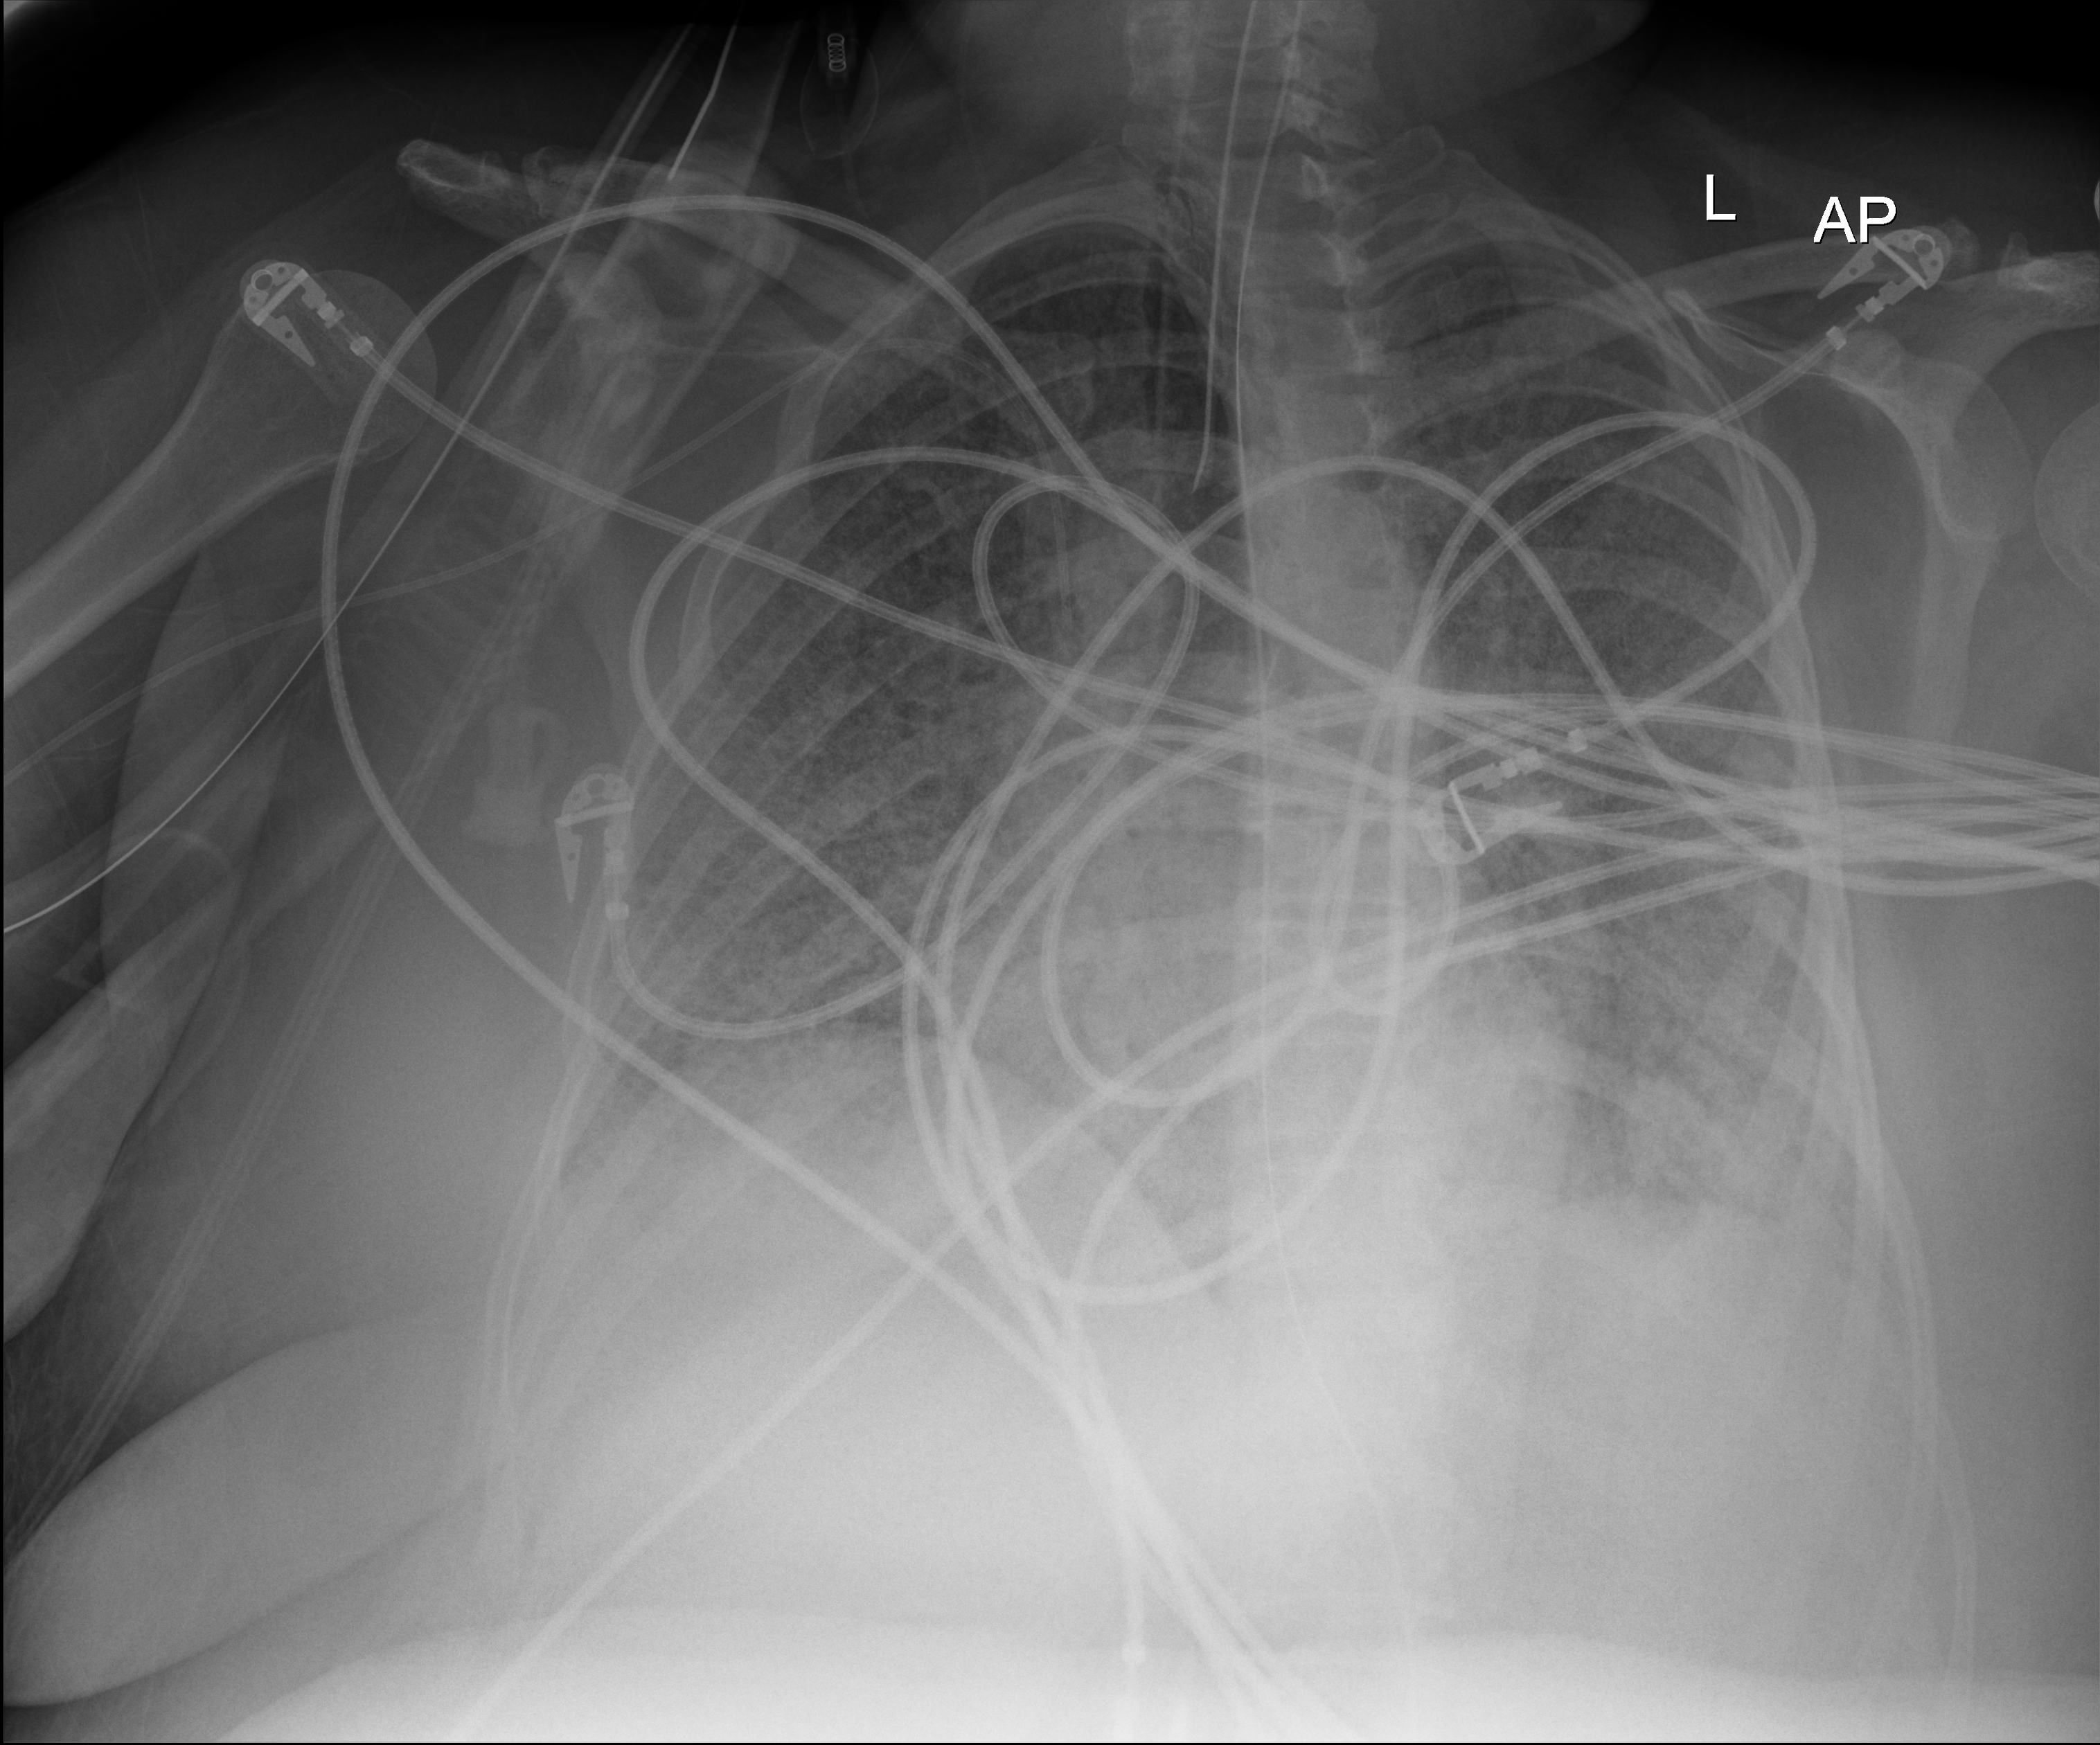
Portable chest radiograph, anteroposterior (AP) projection. Patient hospitalised with COVID-19; female, aged 18–59 years.
Hospital-stay facts (about this admission, not read from this image; timing relative to this image not recorded): admitted to intensive care during this hospital stay: yes.